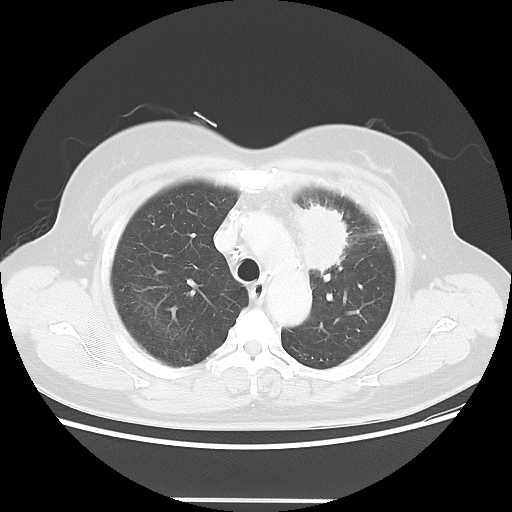
Chest CT, one axial slice; position 41 of 52 along the scan axis; reconstruction kernel LUNG; lung window (W 1500 / L -600 HU); 512 × 512 image matrix, field of view 382 × 382 mm. Patient: female, 52 years. From the clinical record (not read from this slice): clinical TNM (as recorded): T2 N3 M0.
Outlined on this slice (bounding box drawn by a radiologist):
- lung tumour (recorded histology: adenocarcinoma): bounding box <285,195,353,271> (left, top, right, bottom; pixels)